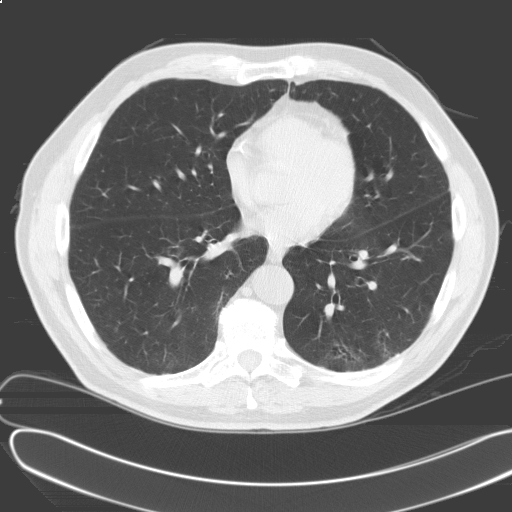
Axial slice from a low-dose chest CT screening exam, baseline annual screen, lung window (W 1500 / L -600 HU), 3.2 mm slice thickness, 512 × 512 image matrix, field of view 389 × 389 mm. Male participant, aged 69 years at enrolment.
Lesion marked by an expert reader, bounding box [x1, y1, x2, y2] px = [204, 122, 234, 151]. The screening reader recorded 2 non-calcified nodules or masses ≥4 mm on this exam (left upper lobe, right lower lobe); which of them this box marks is not recorded. Later outcome: lung cancer diagnosed 450 days after this screen — adenosquamous carcinoma, right upper lobe, poorly differentiated (G3), stage IV (AJCC 6th edition), 30 mm at pathology.